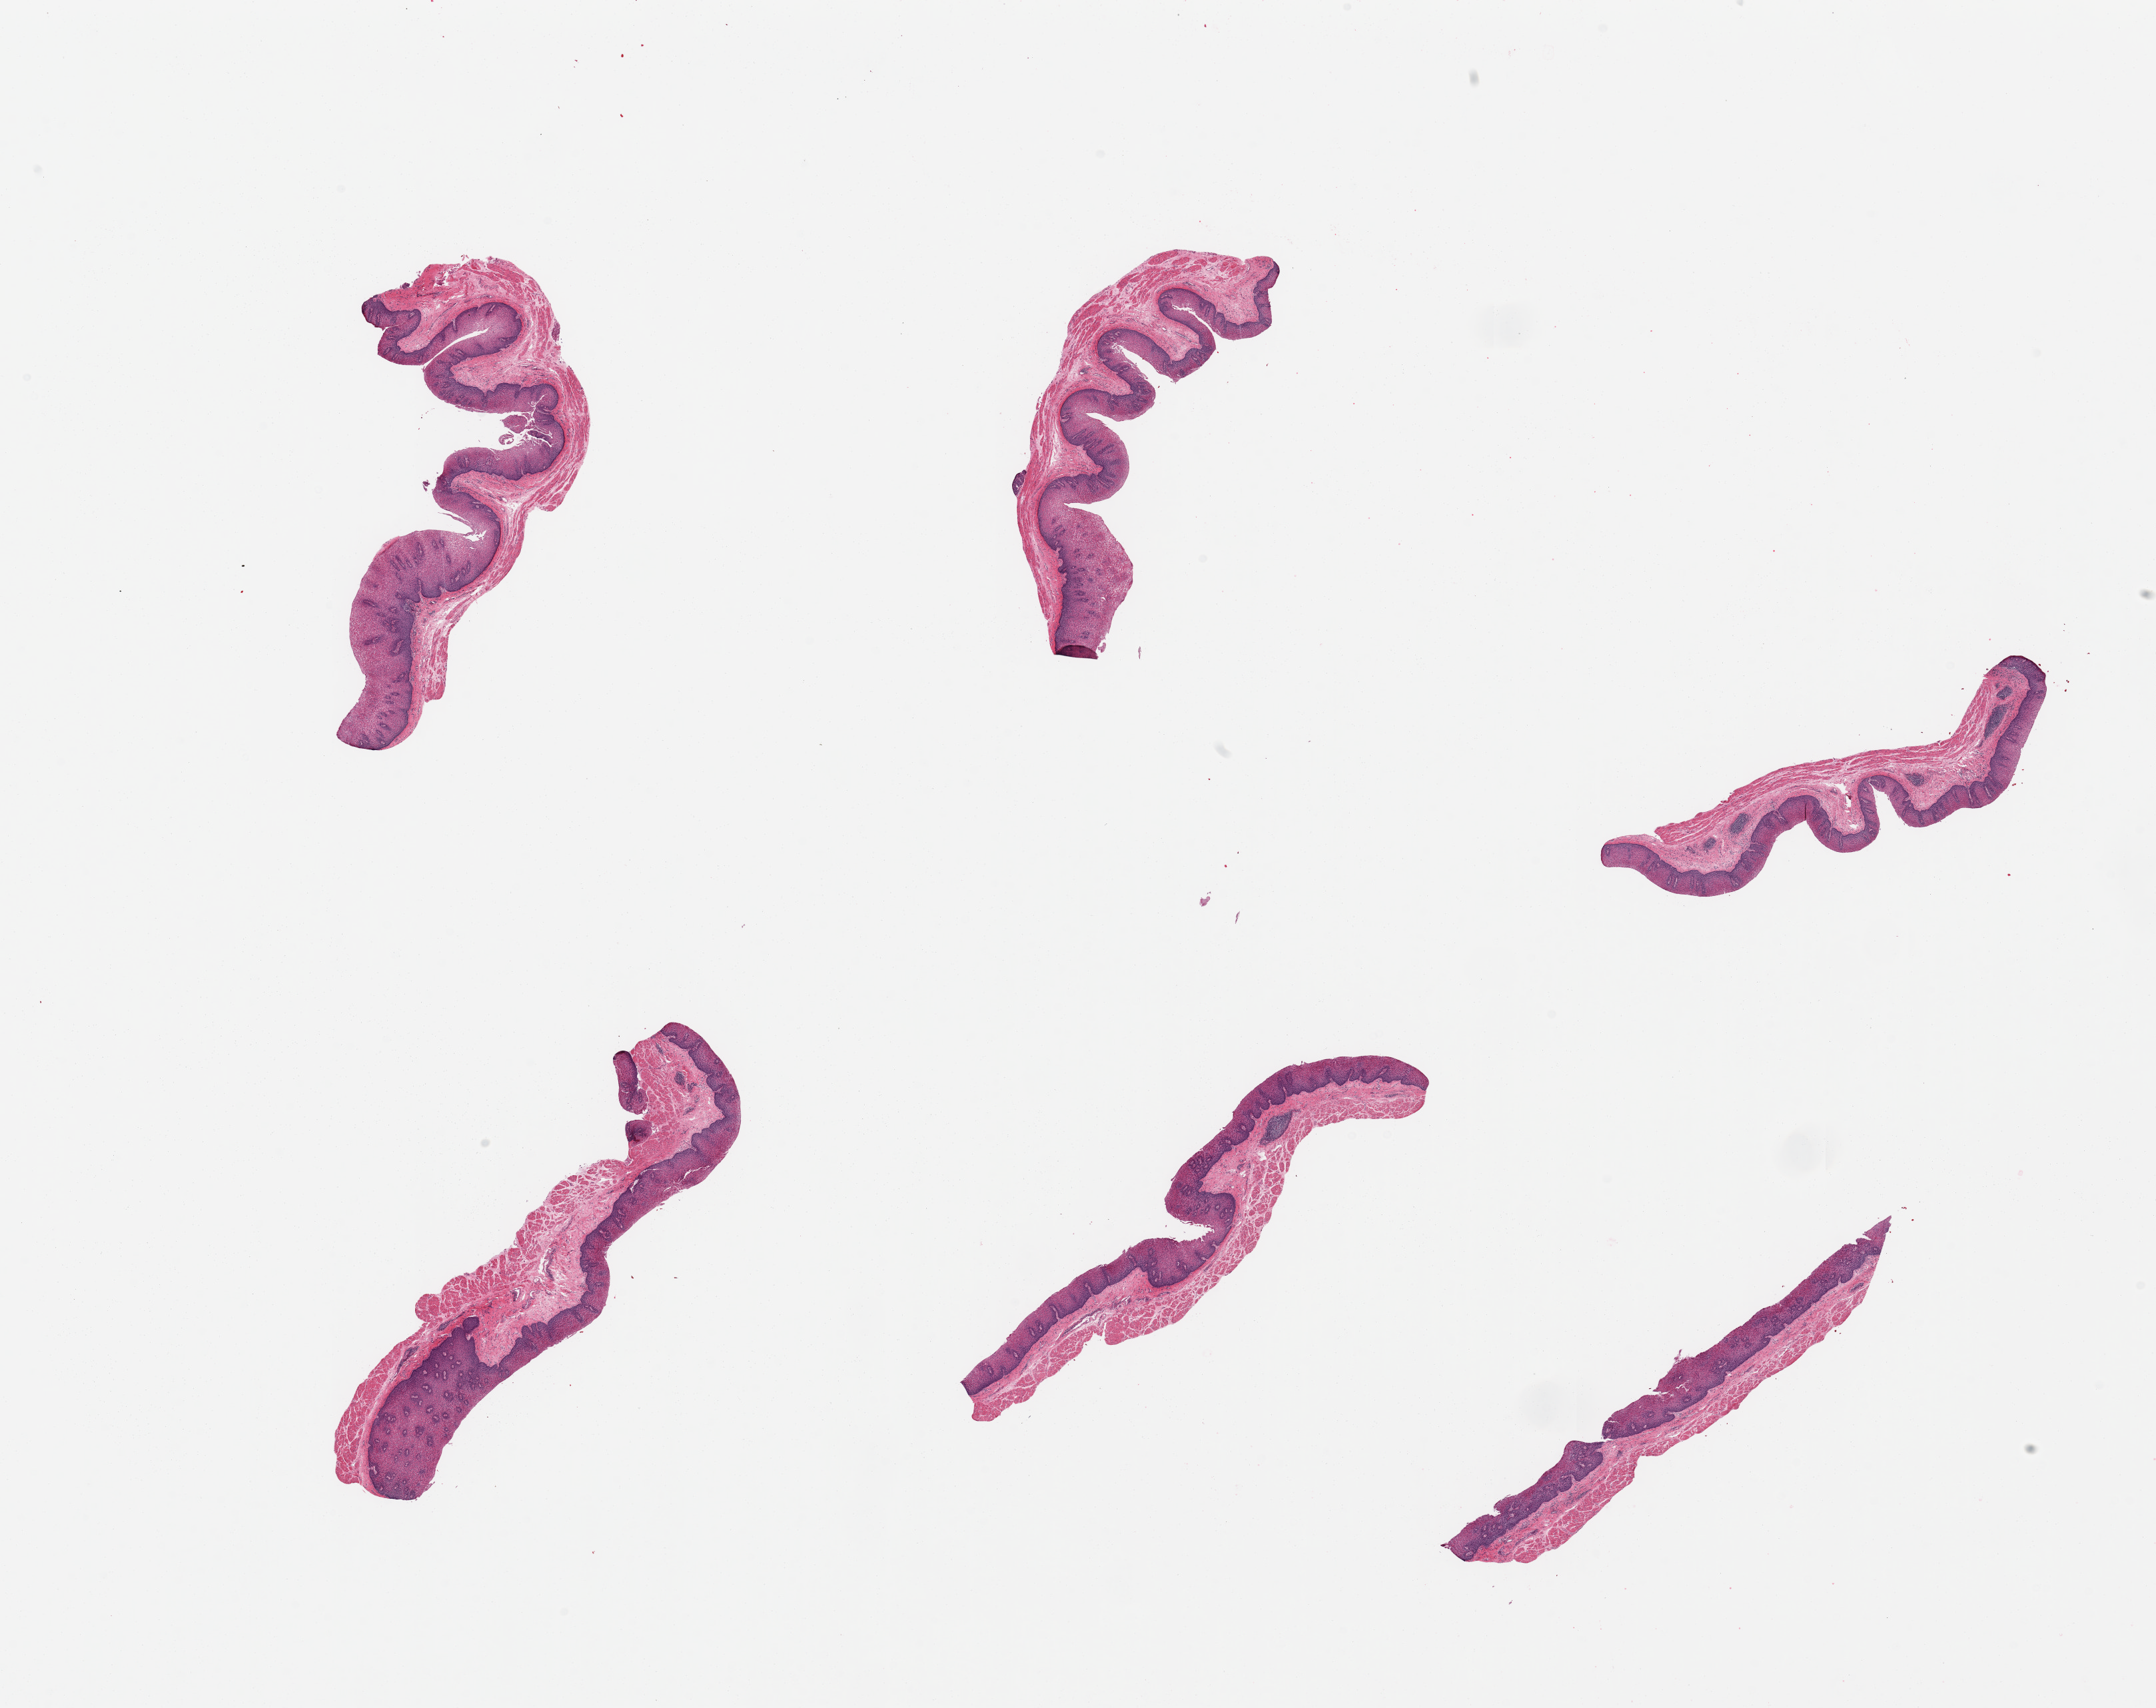
Haematoxylin and eosin whole-slide image — a low-resolution overview of the entire scanned area, about 25.6 x 20.3 mm, PAXgene-fixed paraffin-embedded (PFPE) section, sampled site (target tissue): esophageal mucous membrane, donor tissue sample. Donor sex: female.
Review note (as recorded): 6 pieces; mild chronic esophagitis; focal surface desquamation.